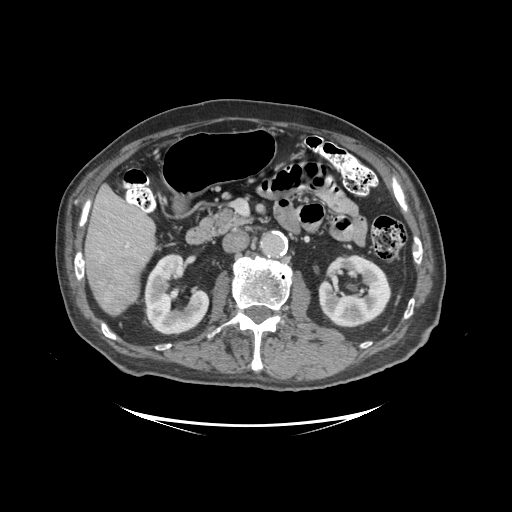
Contrast-enhanced abdominal CT (liver protocol), one axial slice. Position 42 of 99 along the scan axis. Reconstruction kernel STANDARD. 140 kVp. Soft-tissue window (W 400 / L 40 HU). 512 × 512 image matrix, field of view 460 × 460 mm. Case-level facts recorded for this patient, not image findings: diagnosis: hepatocellular carcinoma (patient treated with transarterial chemoembolisation; whether this scan precedes or follows treatment is not stated here); TNM stage (as recorded): Stage-I; Child-Pugh class: A; tumour differentiation: moderately differentiated; tumour nodularity: uninodular.
Structures marked on this image (semi-automatic segmentation, software-assisted and operator-edited):
- liver parenchyma outside the tumour (the mass and vessels are separate outlines, so this box may not span the whole liver): bounding box (x1, y1, x2, y2) in pixels: (84, 185, 154, 315)
- mass: (87, 257, 138, 313)
- liver vessels: (125, 244, 128, 248)